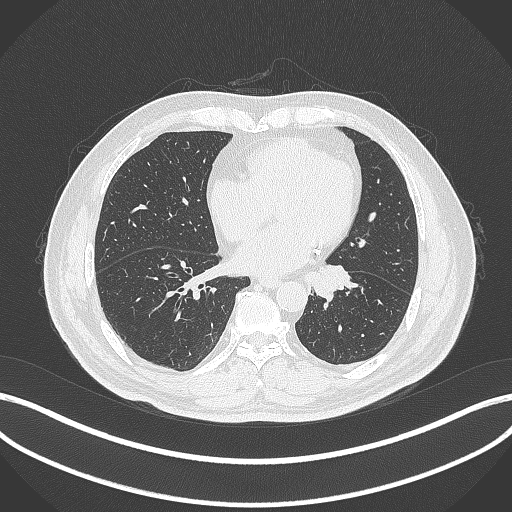
Chest CT, one axial slice. Position 106 of 312 along the scan axis. Reconstruction kernel B70f. 120 kVp. Lung window (W 1500 / L -600 HU). 1 mm slice thickness. 512 × 512 image matrix, field of view 400 × 400 mm. Patient: male, 71 years. From the clinical record (not read from this slice): clinical TNM (as recorded): T1b N0 M0.
Outlined on this slice (rectangle marked by the reading radiologist):
- lung tumour (recorded histology: squamous cell carcinoma): box from (x=308, y=260) to (x=353, y=304) px